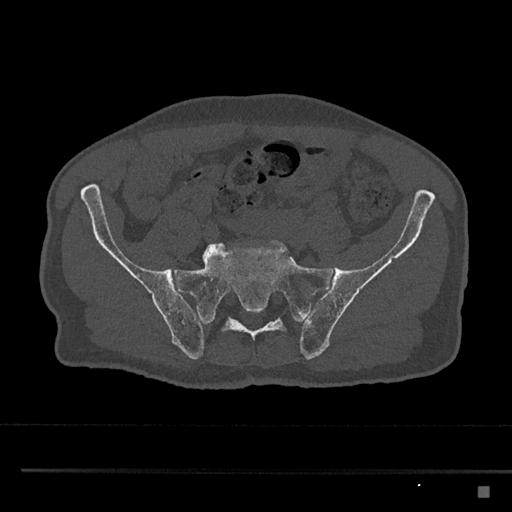
CT including the spine, one axial slice. Slice 521 of 797 in the series (ordered by position). Reconstruction kernel Br40s/3. Bone window (W 1800 / L 400 HU). 512 × 512 image matrix, field of view 391 × 391 mm. Male patient, age 59 years. From the clinical record (not read from this slice): primary cancer: prostate.
Structures marked on this image (semi-automatically segmented with operator editing):
- L5 vertebra: bounding box (x1, y1, x2, y2) in pixels: (202, 243, 267, 262)